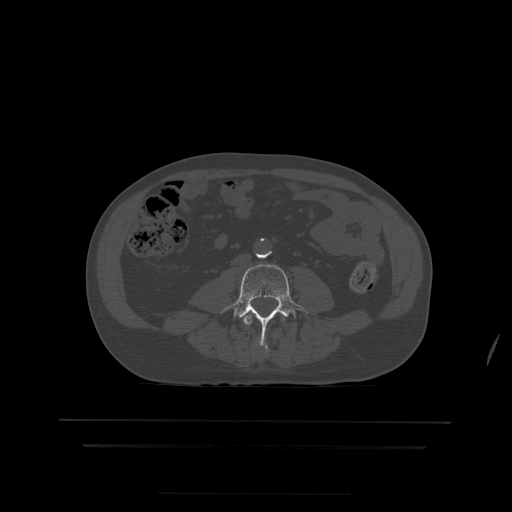
CT including the spine, one axial slice; slice 99 of 522 in the series (ordered by position); bone window (W 1800 / L 400 HU); 1.25 mm slice thickness; 512 × 512 image matrix, field of view 436 × 436 mm. Patient age 68 years. From the clinical record (not read from this slice): primary cancer: urothelial.
Annotated regions visible in this slice (semi-automatically segmented with operator editing):
- L3 vertebra: bounding box [x1, y1, x2, y2] px = [243, 315, 285, 351]
- L4 vertebra: [221, 264, 308, 347]